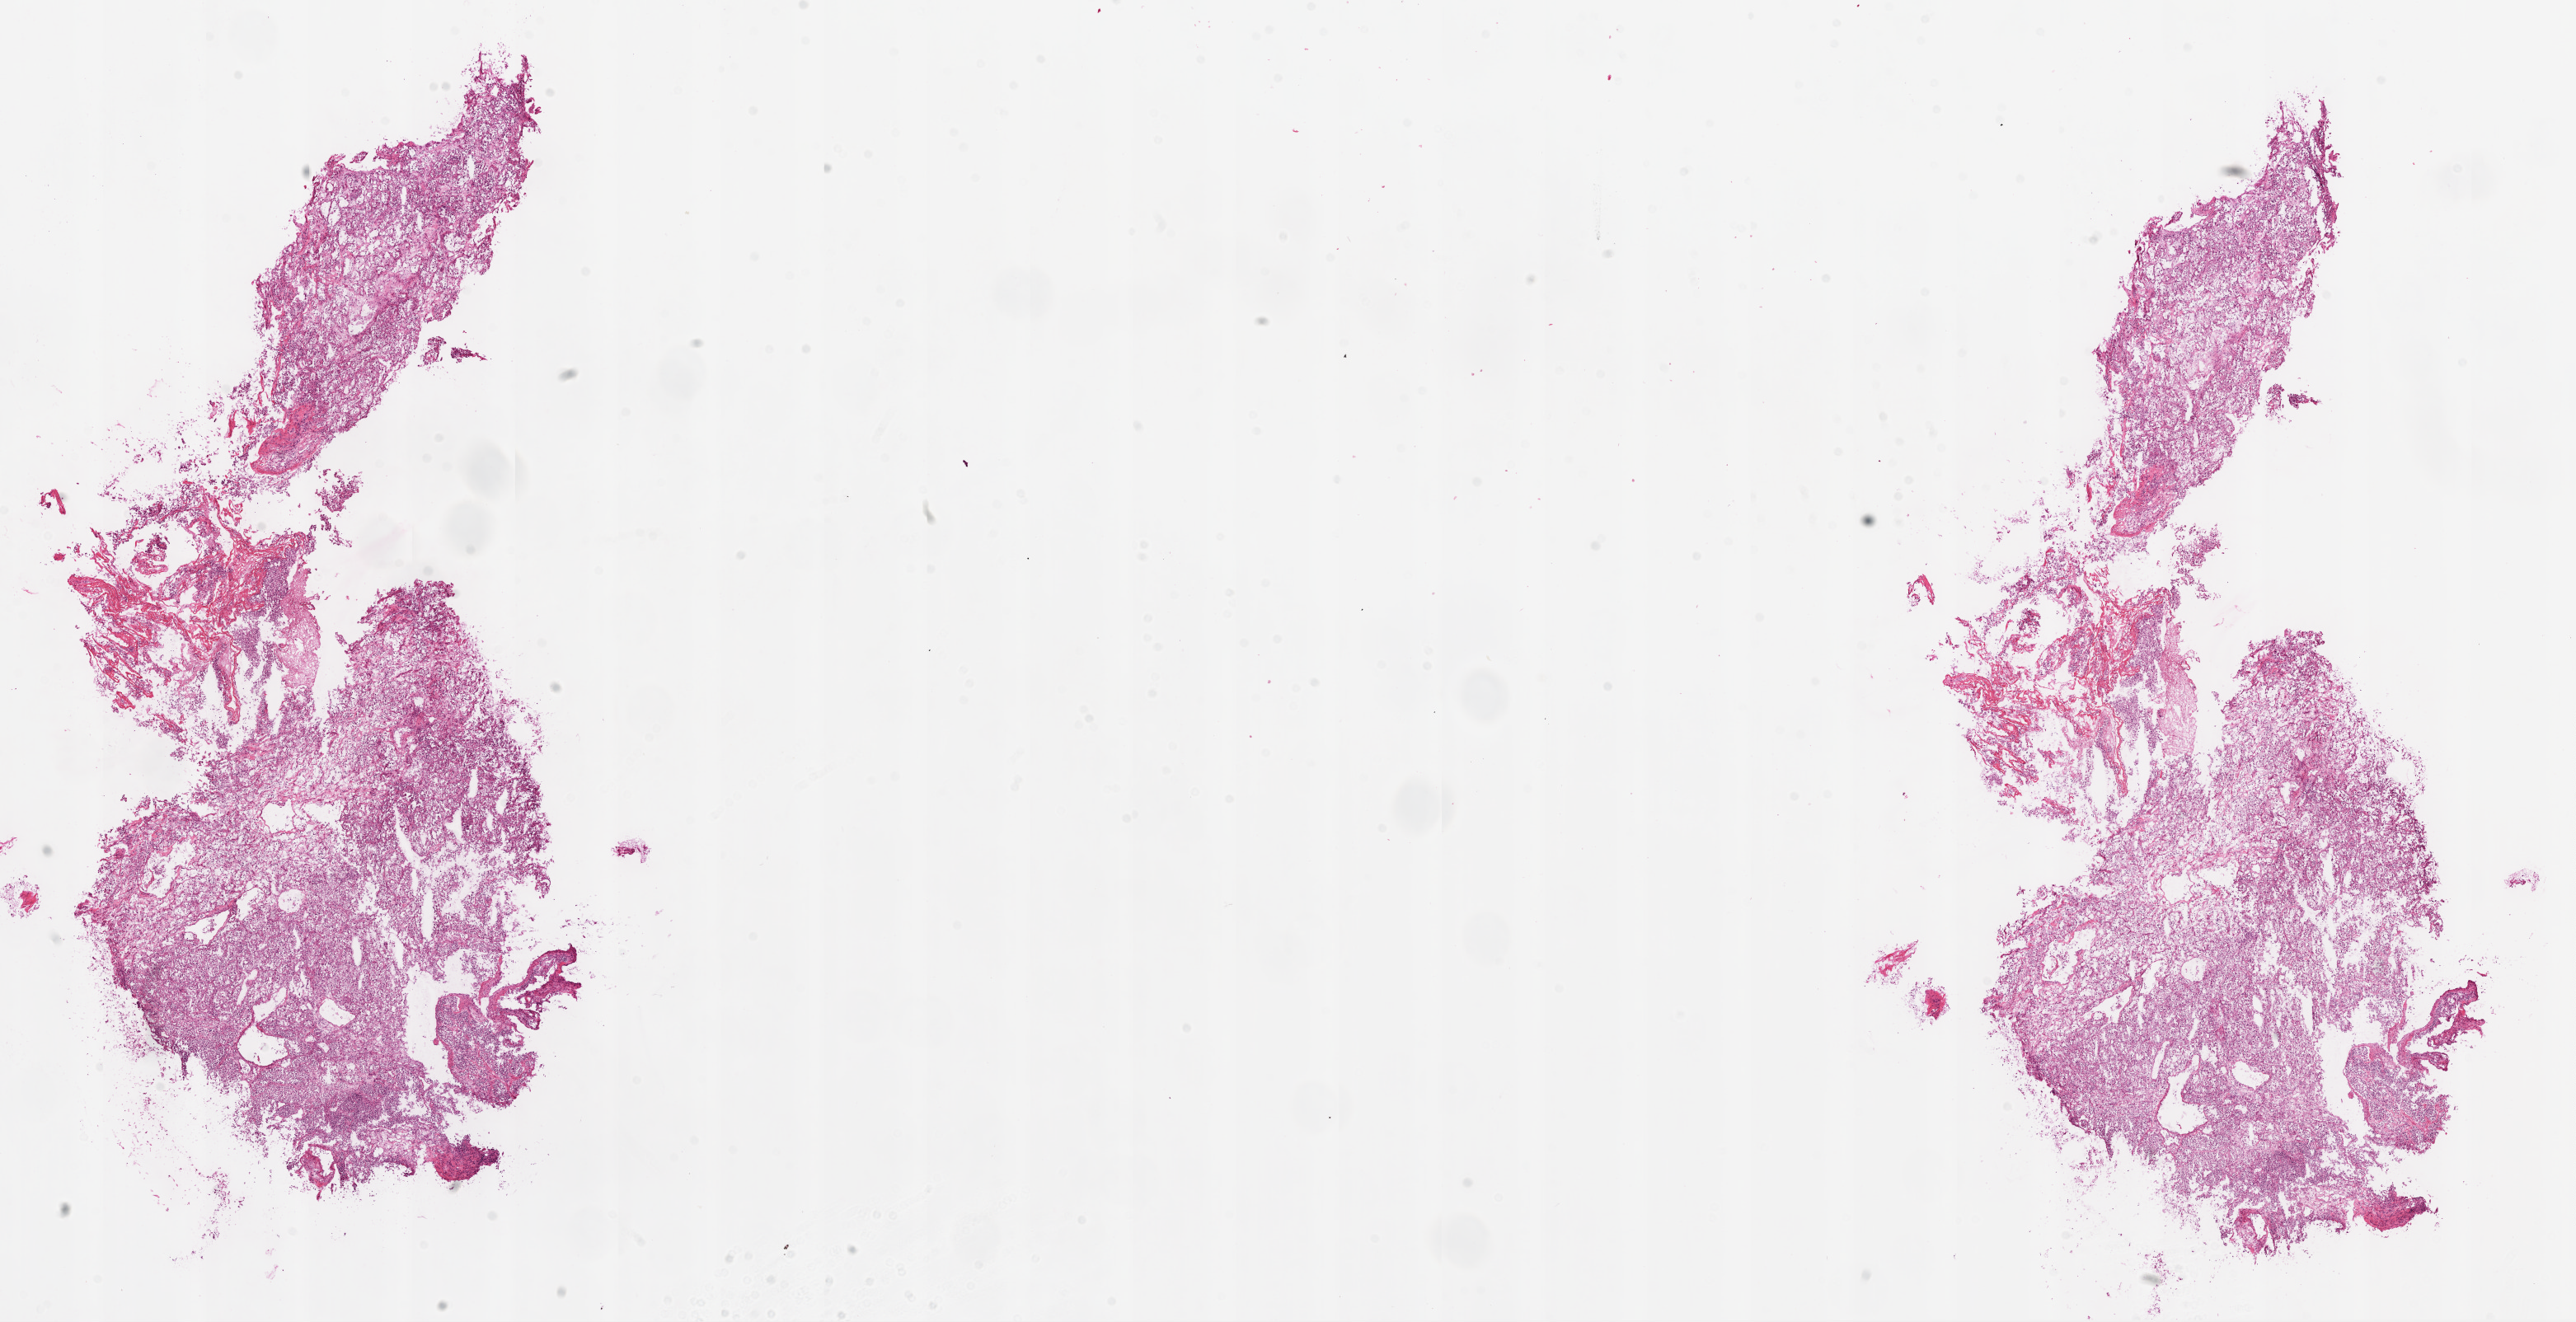
H&E-stained whole-slide image, shown as a low-resolution overview of the whole scanned area (about 25.1 x 12.9 mm). Frozen section from the top of the tissue portion. Kidney, primary tumour sample. Male patient; age at initial diagnosis 26 years. Histologic grade: G2 (moderately differentiated). Composition of this section per pathologist review: tumour cells 85%, tumour nuclei 80%, normal cells 0%, stromal cells 15%, necrosis 0%.
* AJCC pathologic stage: I
* histologic diagnosis: Clear cell adenocarcinoma, NOS
* TNM: T1a NX M0
* laterality: right